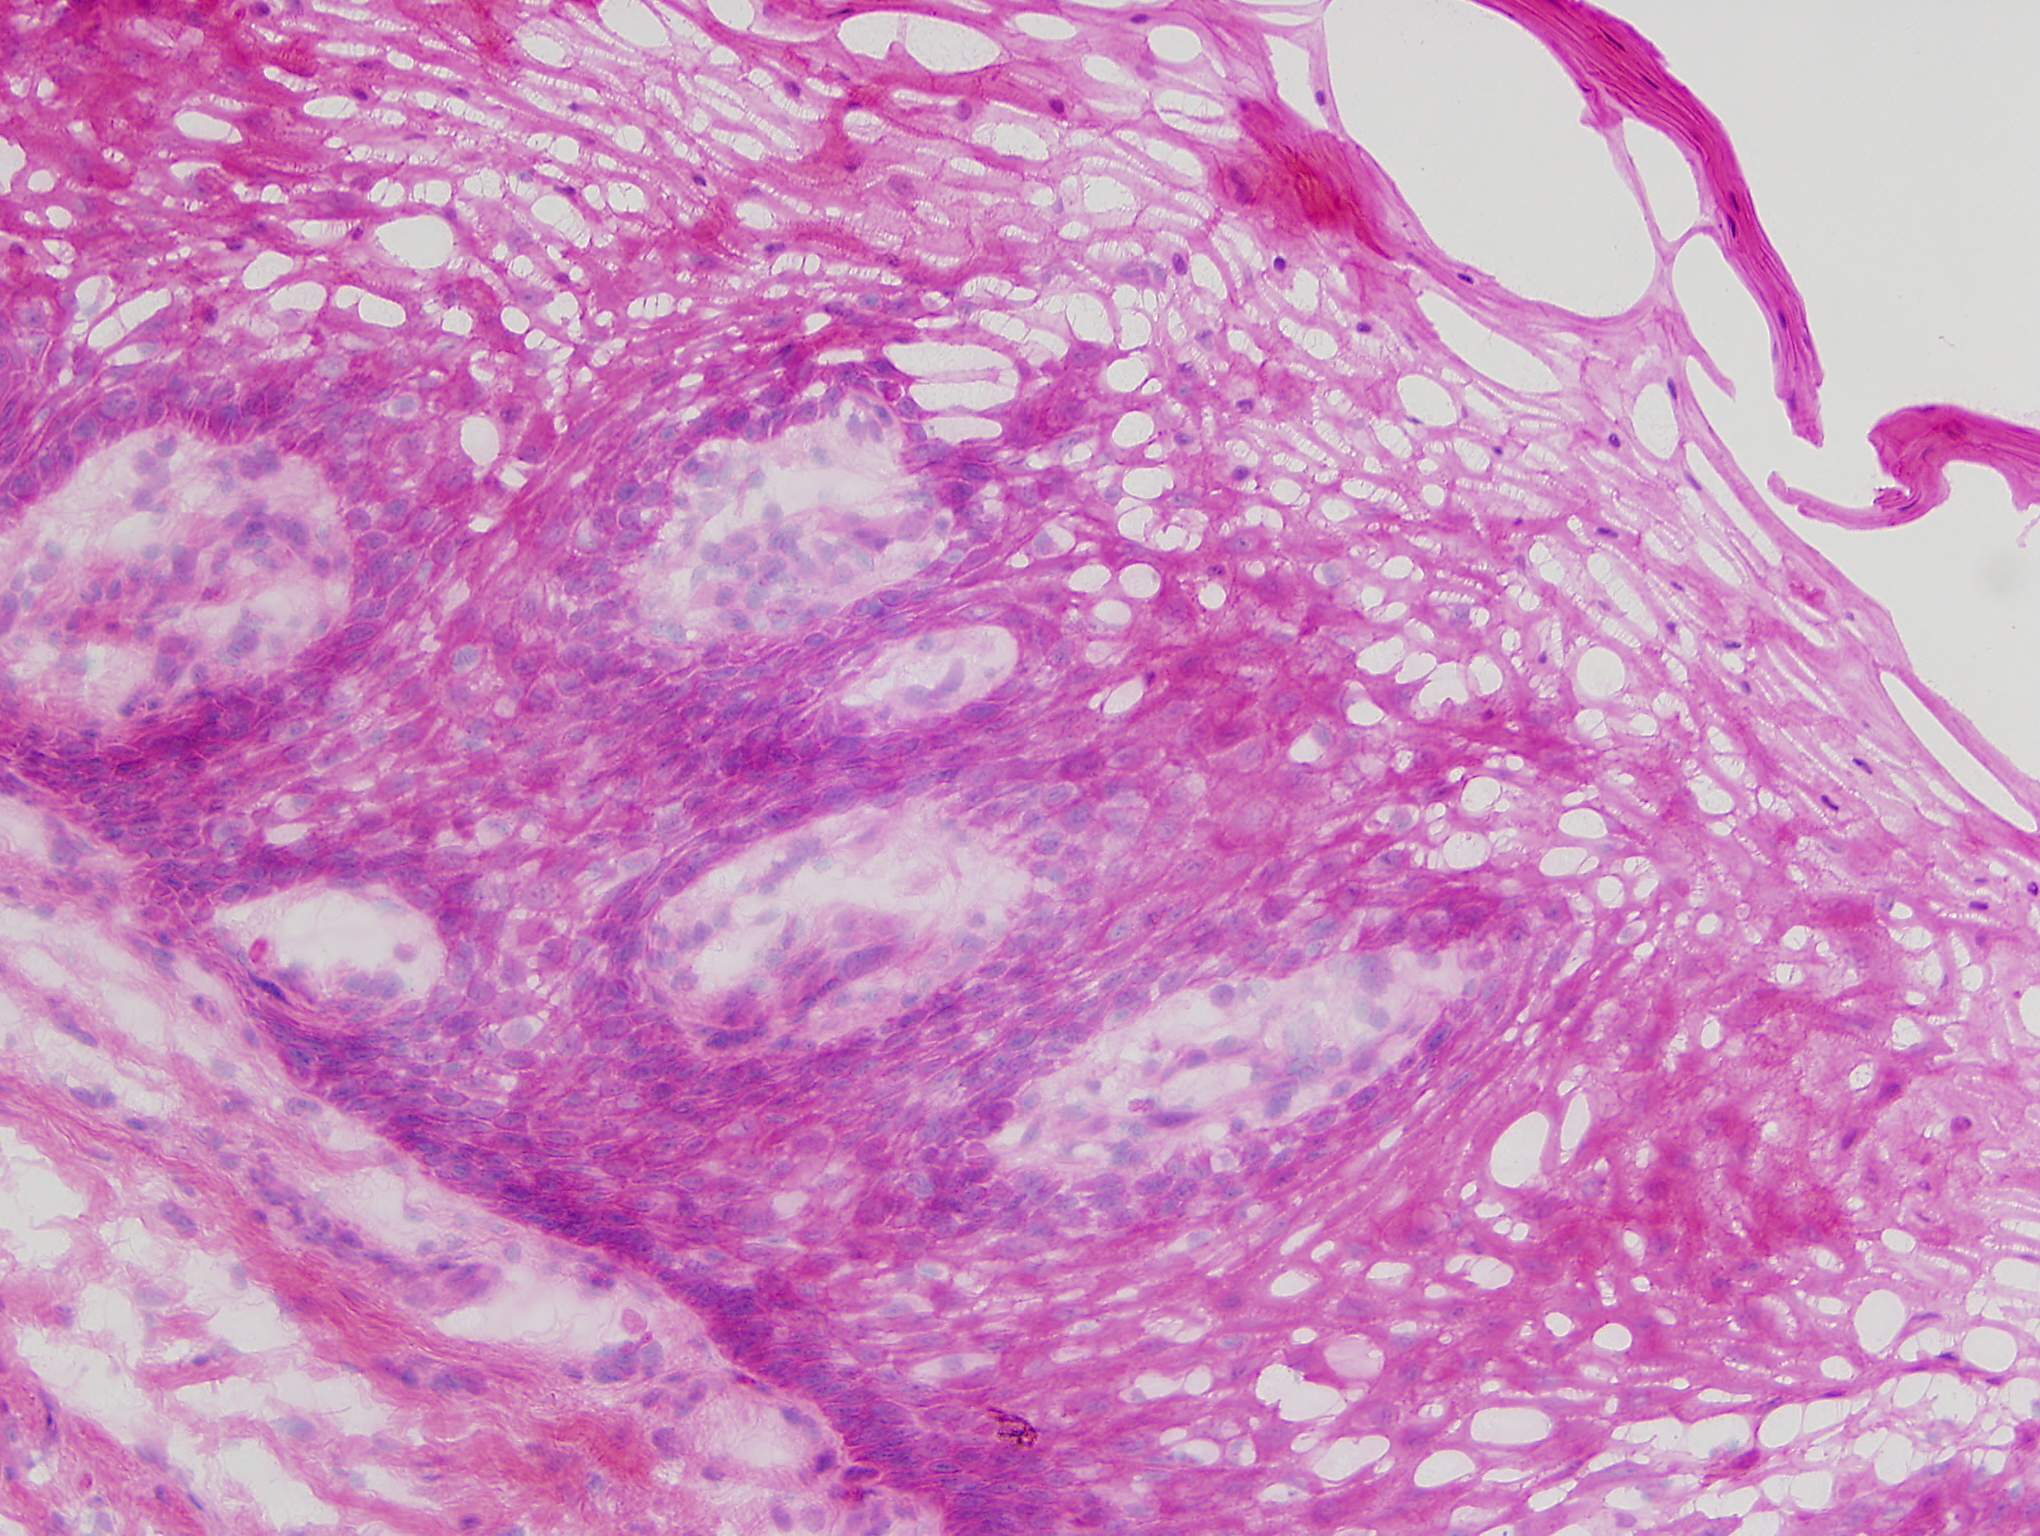
Single-field Hematoxylin and eosin (H&E) stained photomicrograph — roughly 1.0 x 0.8 mm in extent; frozen section from the top of the tissue portion; head and neck, solid tissue normal (non-tumour tissue) sample. Female, age 29 years at initial diagnosis. Infiltration values recorded for this section: lymphocyte infiltration 1%, monocyte infiltration 1%, neutrophil infiltration 0%.
• this section: solid tissue normal sample (biorepository sample class)
• patient diagnosis: Squamous cell carcinoma, NOS (overlapping lesion of lip, oral cavity and pharynx)